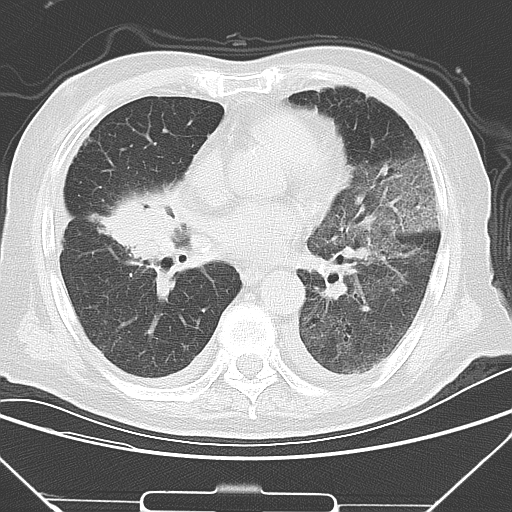
Chest CT, one axial slice; slice 15 of 43 in the series (ordered by position); lung window (W 1500 / L -600 HU); 5 mm slice thickness; 512 × 512 image matrix, field of view 343 × 343 mm. Male patient, age 85 years. From the clinical record (not read from this slice): clinical TNM (as recorded): T4 N3 M2.
Annotated regions visible in this slice (bounding box drawn by a radiologist):
- lung tumour (recorded histology: squamous cell carcinoma): bounding box [x1, y1, x2, y2] px = [95, 183, 187, 271]